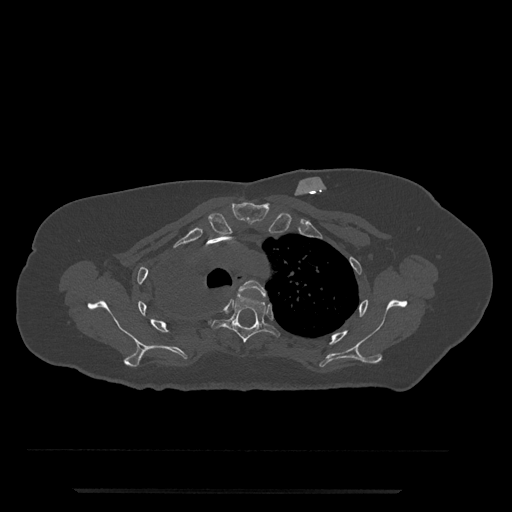
CT including the spine, one axial slice; position 596 of 797 along the scan axis; bone window (W 1800 / L 400 HU); 0.5 mm slice thickness; 512 × 512 image matrix, field of view 440 × 440 mm. Female patient, age 51 years. From the clinical record (not read from this slice): primary cancer: neuro.
Annotated regions visible in this slice (semi-automatically segmented with operator editing):
- T3 vertebra: bounding box <238,280,266,298> (left, top, right, bottom; pixels)
- T4 vertebra: <211,295,280,343>